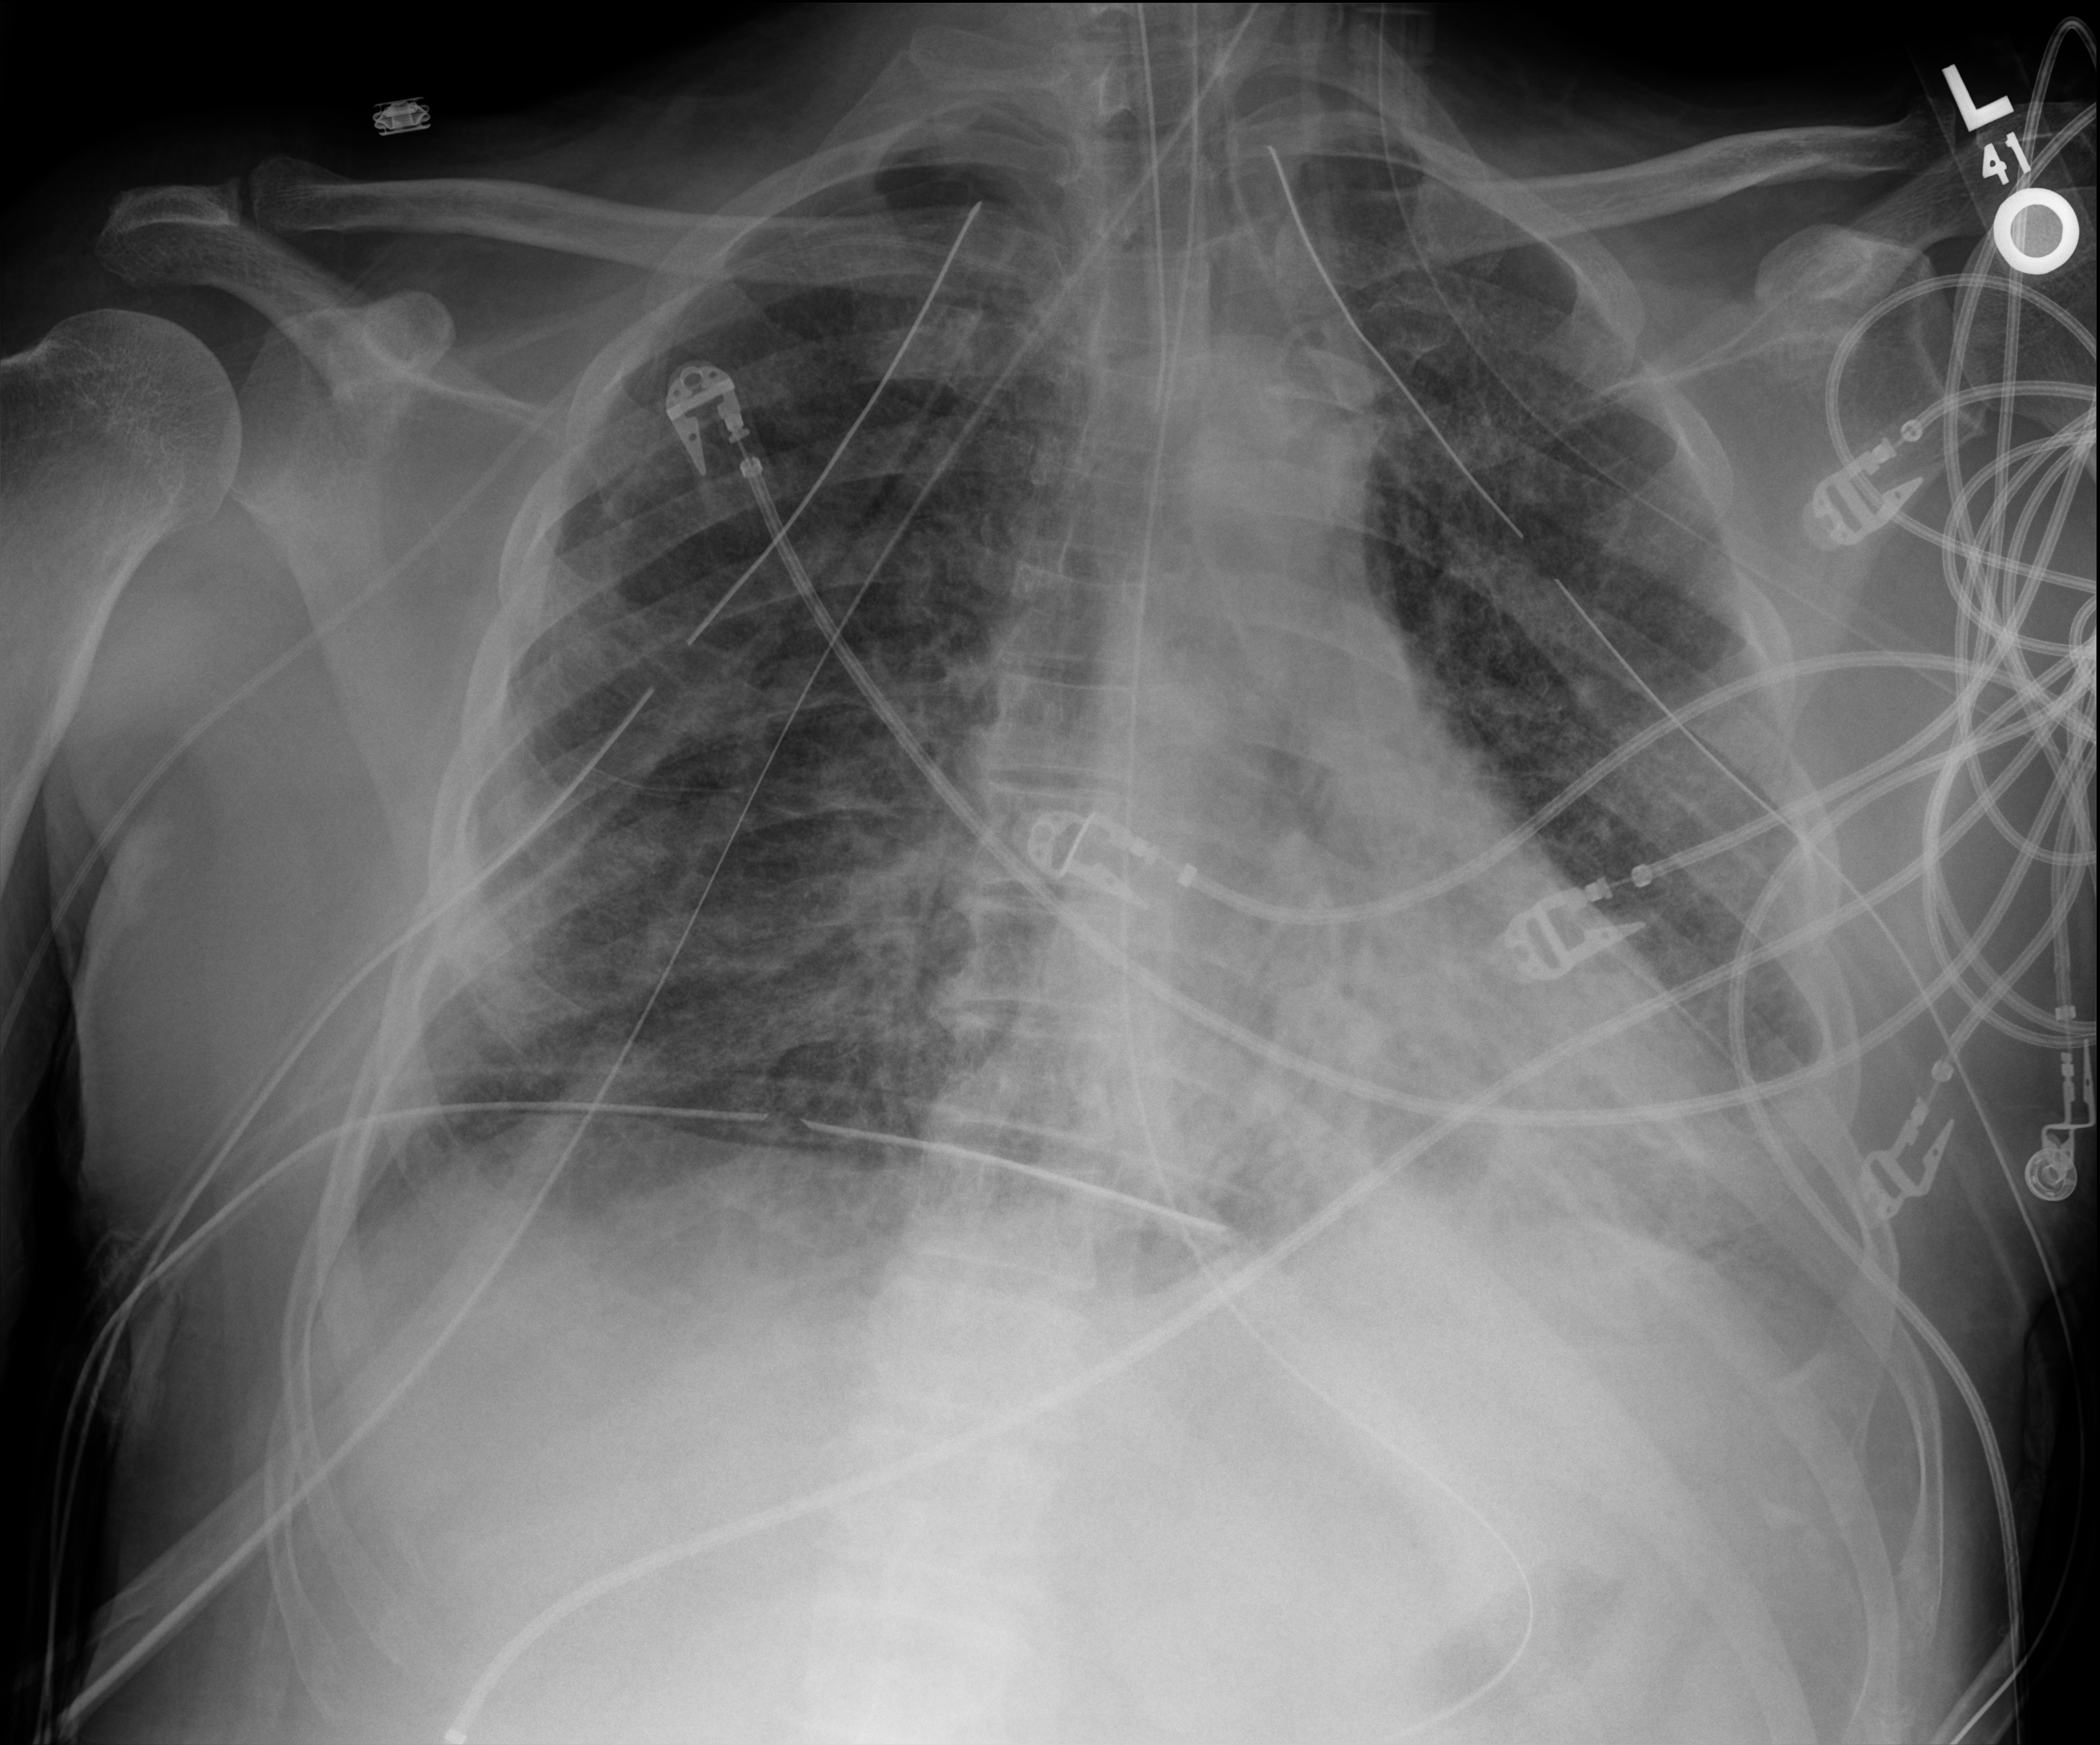
Chest X-ray (portable), anteroposterior (AP) projection. Male patient hospitalised with COVID-19, age 18–59 years.
Admission-level facts for this patient (not findings on this image; timing relative to this image not recorded): COPD (admission record): no; admitted to intensive care during this hospital stay: yes.